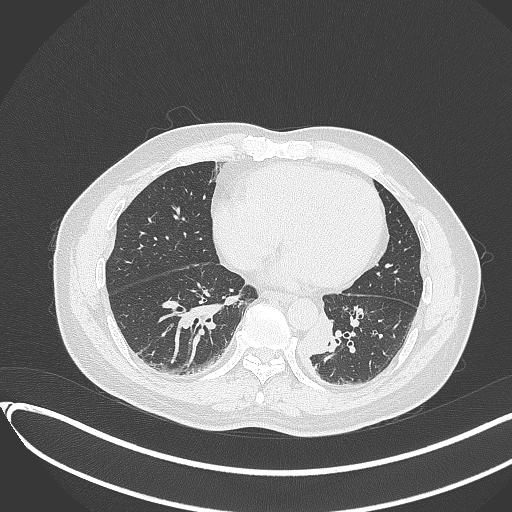
Chest CT, one axial slice. Position 118 of 417 along the scan axis. 120 kVp. Lung window (W 1500 / L -600 HU). 512 × 512 image matrix, field of view 400 × 400 mm. Patient: male, 54 years. Case-level facts recorded for this patient, not image findings: clinical TNM (as recorded): T3 N0 M0.
Outlined on this slice (rectangle marked by the reading radiologist):
- lung tumour (recorded histology: squamous cell carcinoma): bounding box [x1, y1, x2, y2] px = [301, 305, 335, 363]